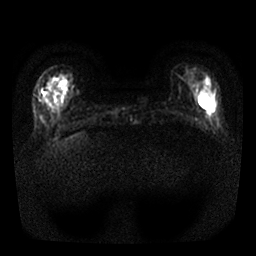
Breast MRI, one axial slice; diffusion-weighted series; image 2 of 4 stored at this slice position (different b-values; order by instance number); 1.5 T; 4 mm slice thickness; 256 × 256 image matrix, field of view 310 × 310 mm. Female patient.
Structures marked on this image (manually delineated by an expert):
- tumour on diffusion-weighted imaging: bounding box <44,98,46,101> (left, top, right, bottom; pixels)